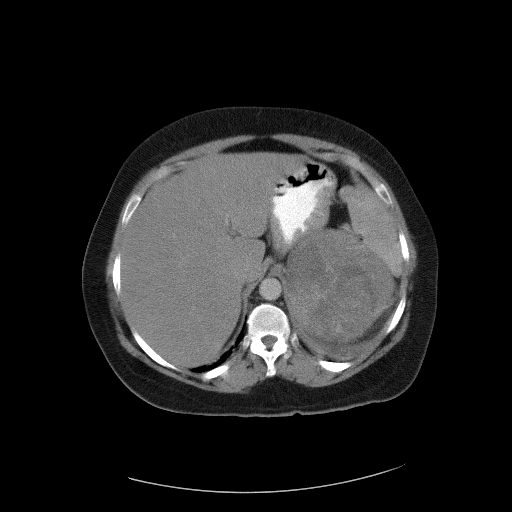
Contrast-enhanced abdominal CT, one axial slice. Position 77 of 90 along the scan axis. 120 kVp. Intravenous contrast given. Soft-tissue window (W 400 / L 40 HU). 512 × 512 image matrix. Patient: female, 55 years. Case-level facts recorded for this patient, not image findings: diagnosis: adrenocortical carcinoma; tumour side: left adrenal.
Outlined on this slice (semi-automatic segmentation, software-assisted and operator-edited):
- mass: box from (x=289, y=230) to (x=390, y=338) px